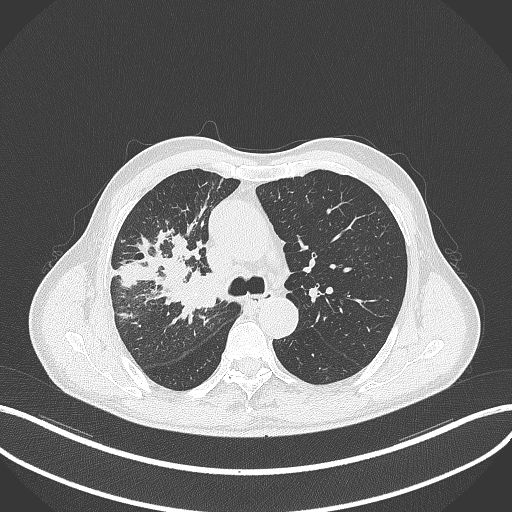
Chest CT, one axial slice; reconstruction kernel B70f; 120 kVp; lung window (W 1500 / L -600 HU); 1 mm slice thickness; 512 × 512 image matrix, field of view 400 × 400 mm. Male patient, age 69 years. From the clinical record (not read from this slice): clinical TNM (as recorded): T2a N0 M0.
Structures marked on this image (bounding box drawn by a radiologist):
- lung tumour (recorded histology: adenocarcinoma): bounding box <180,269,219,314> (left, top, right, bottom; pixels)